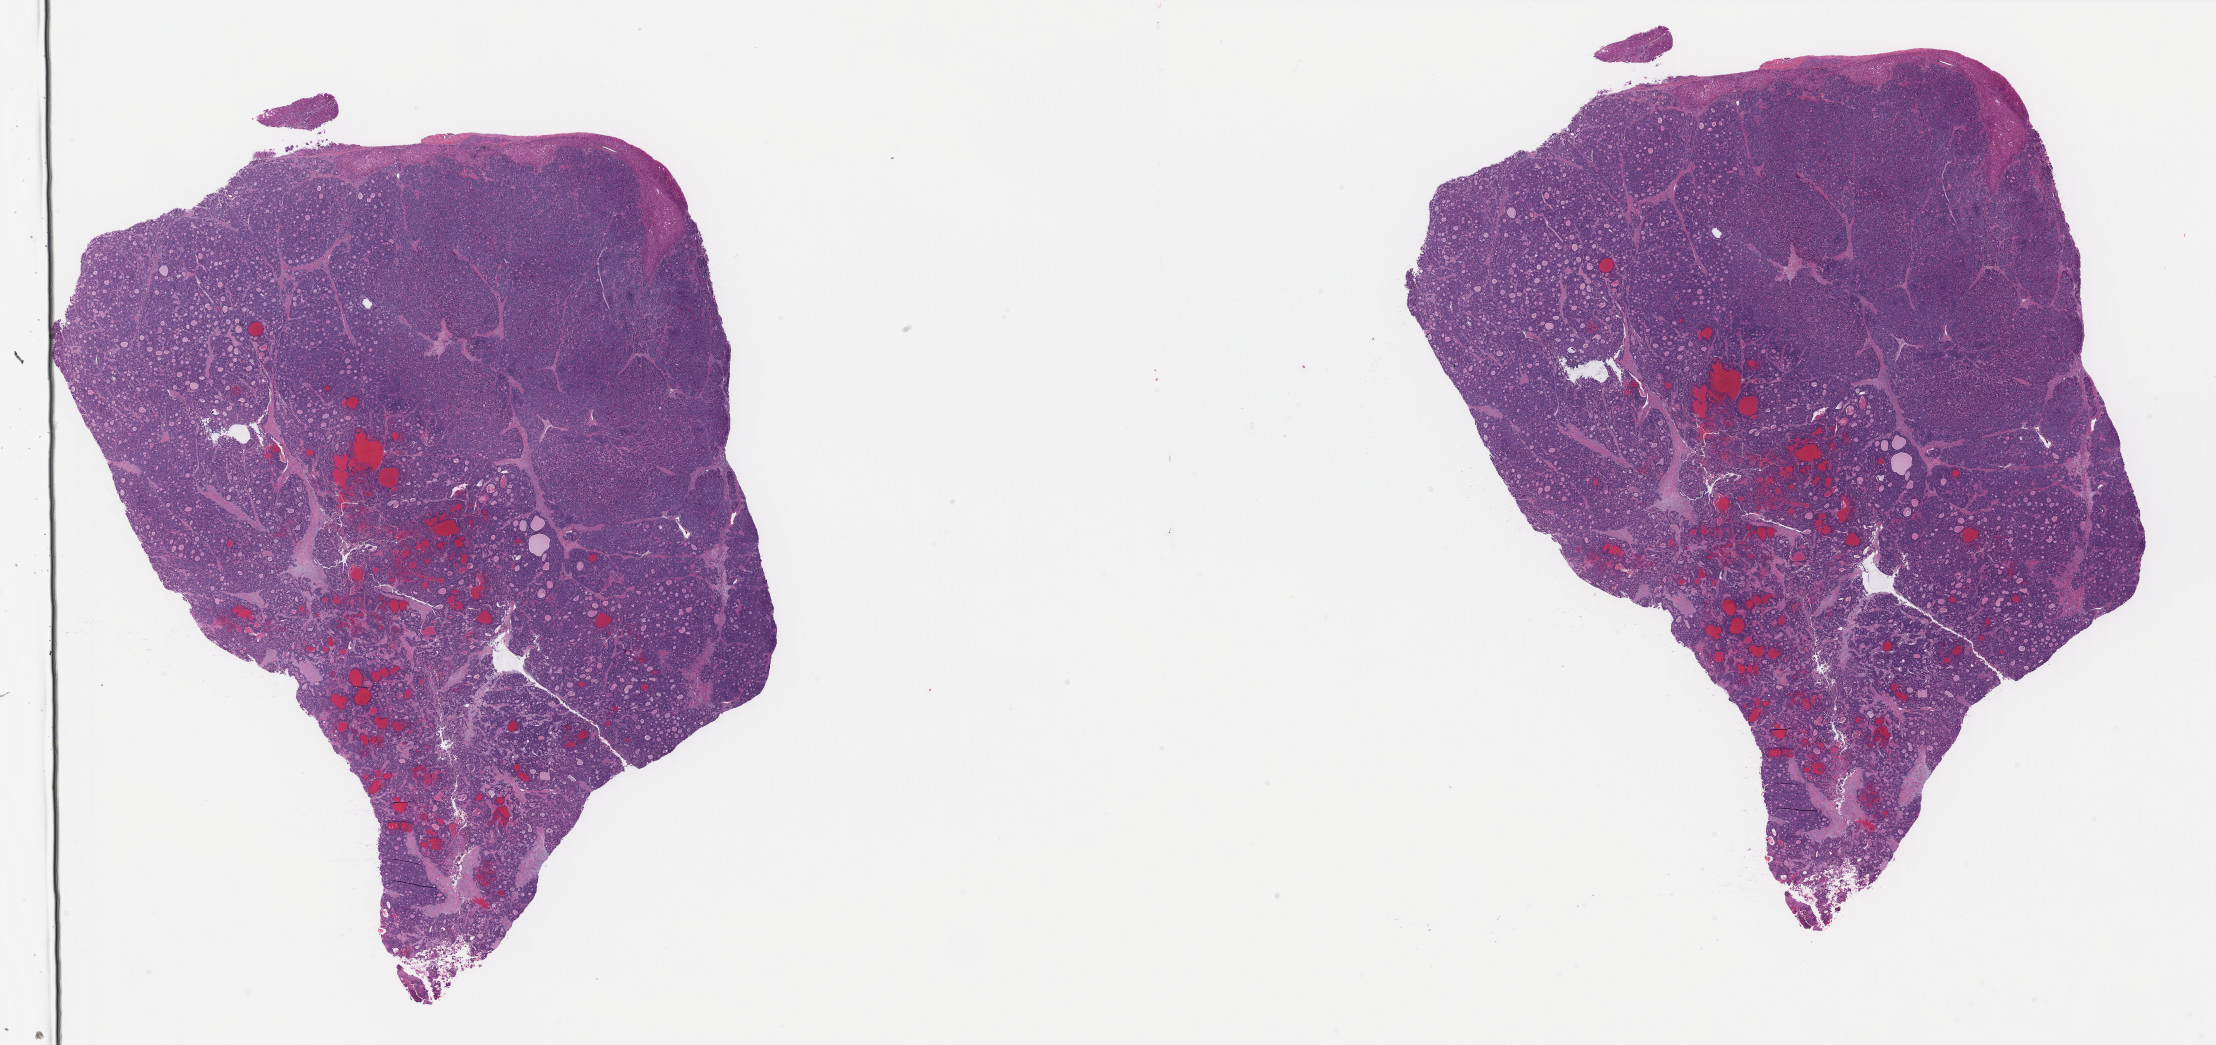
Whole-slide histology image, Hematoxylin and eosin (H&E) stained, whole scanned area (about 35.1 x 16.5 mm, slide scanned at 40x) shown as a low-resolution overview. FFPE section. Bile duct, primary tumour sample. Female, age 41 years at initial diagnosis.
Diagnosis: Cholangiocarcinoma.